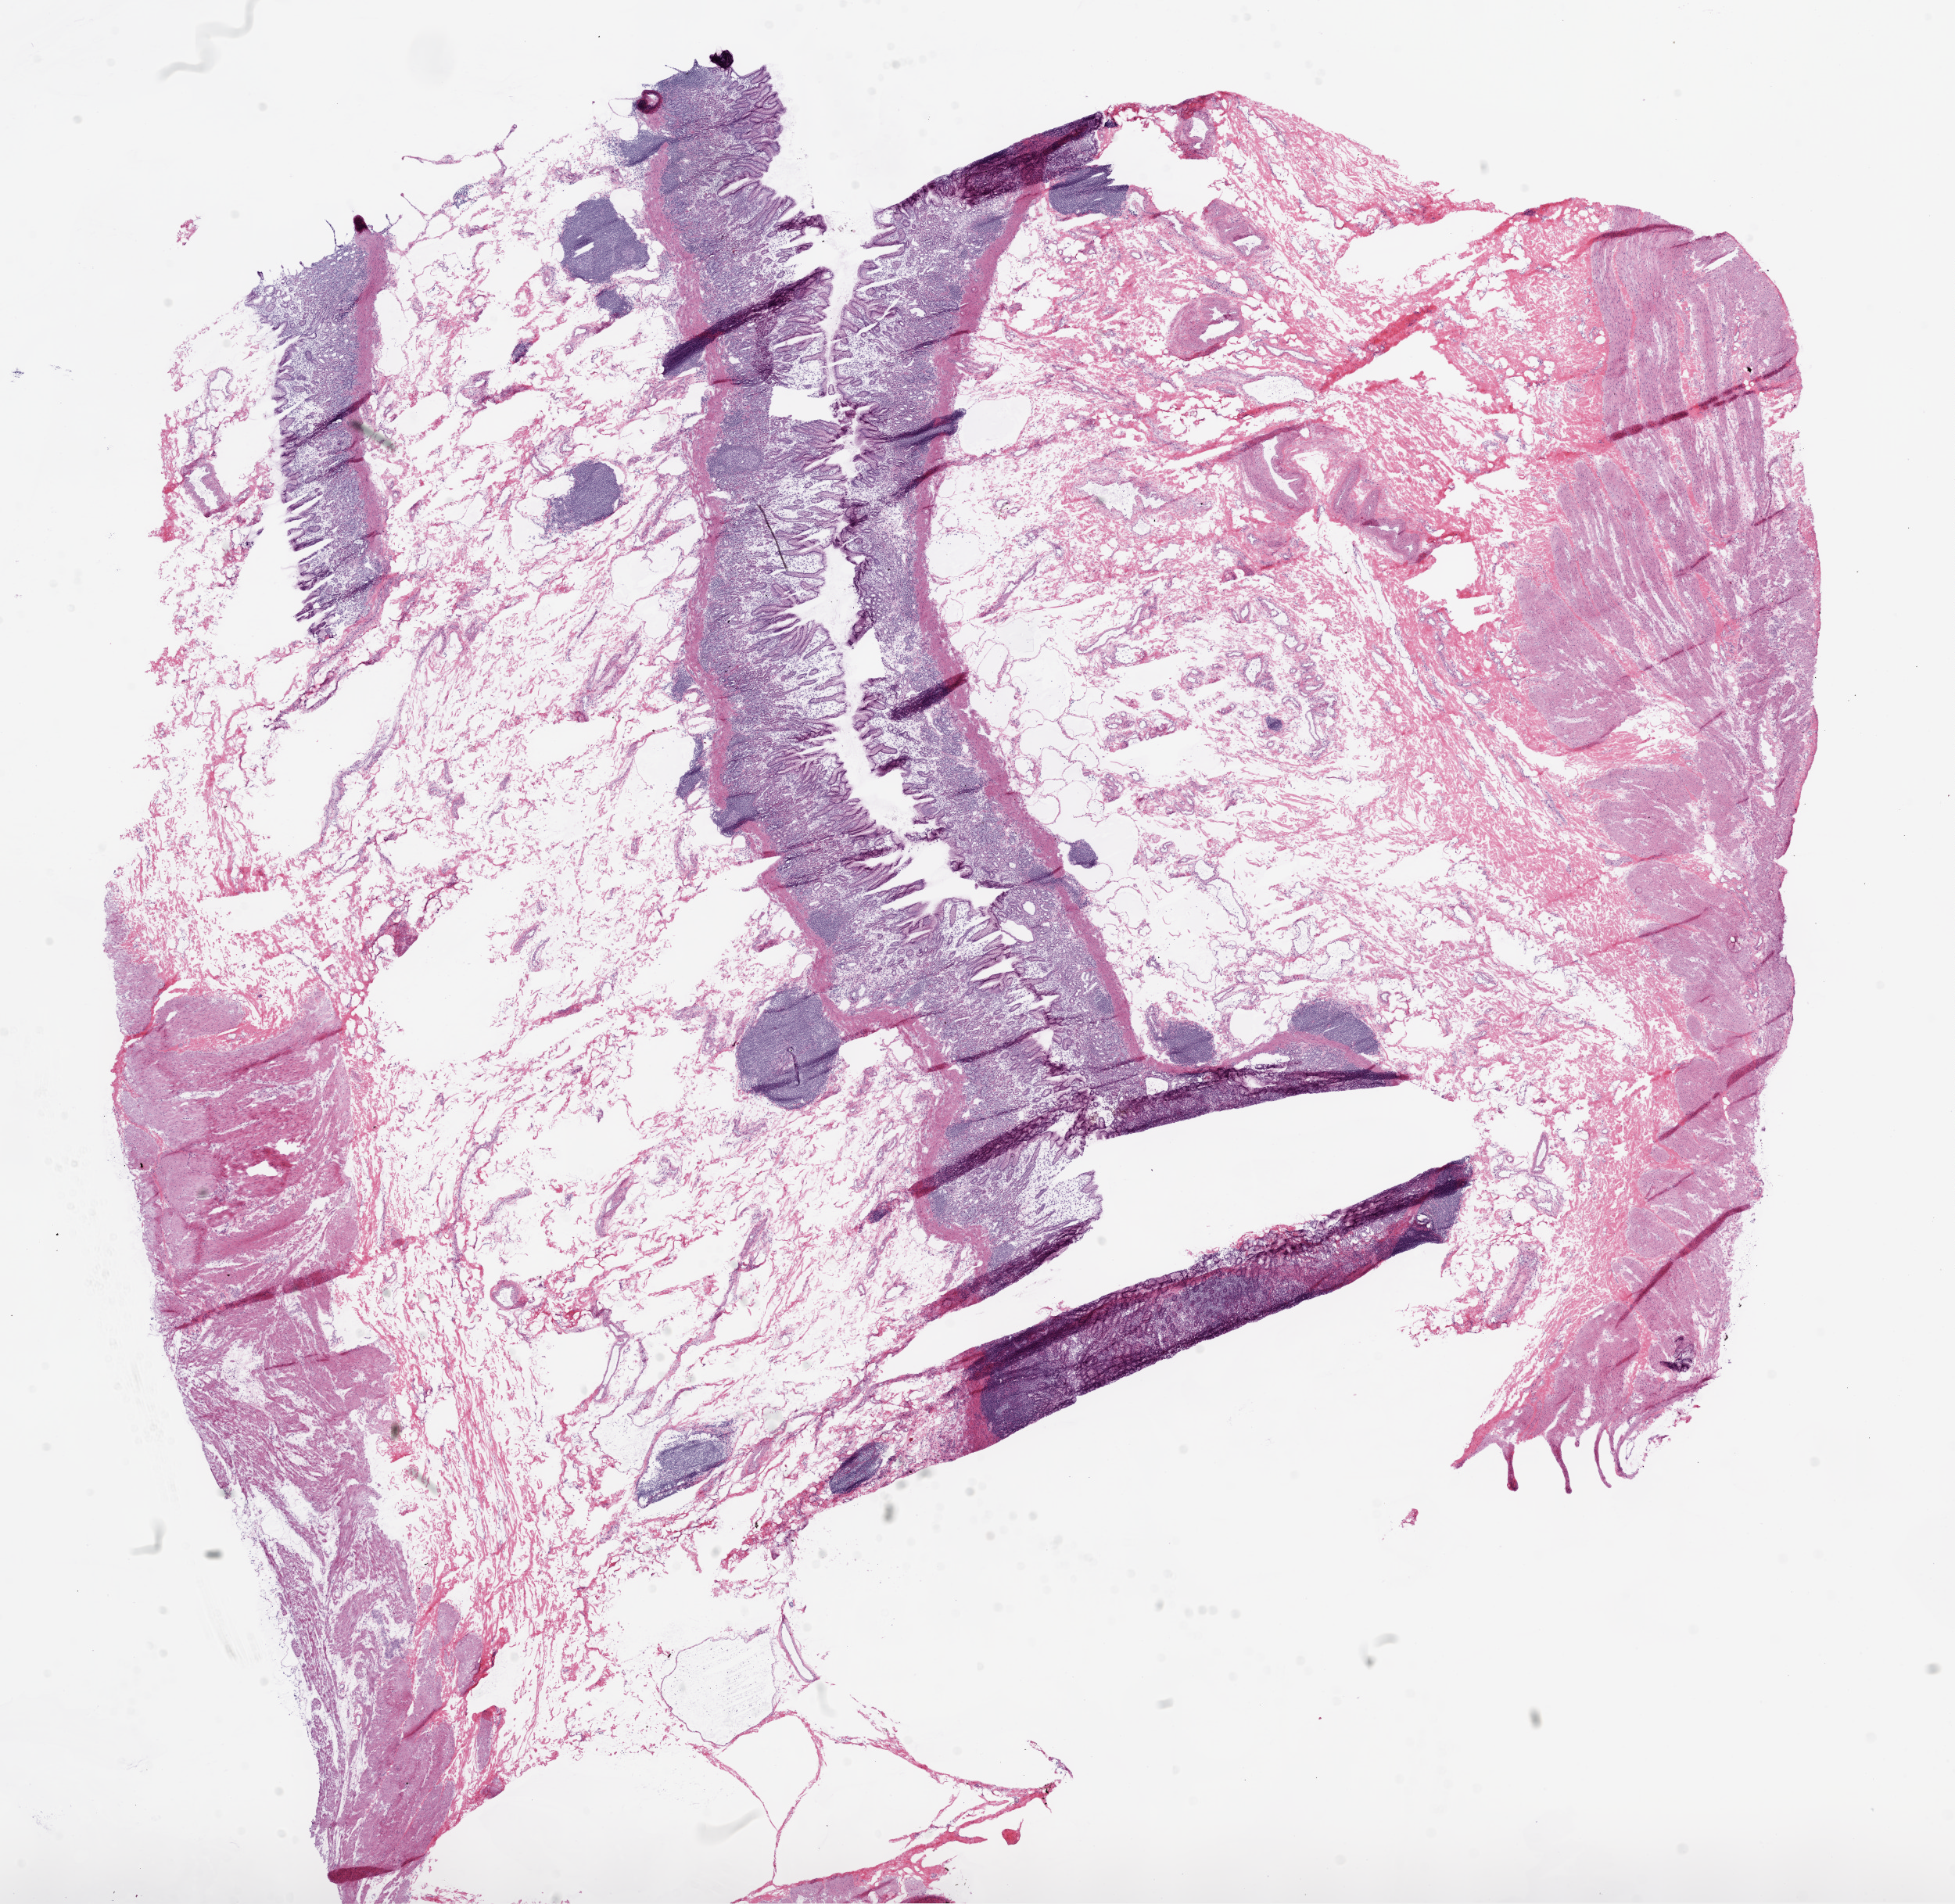
Digitized Hematoxylin and eosin (H&E) stained tissue section (whole slide), whole scanned area (about 20.1 x 19.5 mm, from a 20x scan) shown as a low-resolution overview; frozen section from the bottom of the tissue portion; sample: solid tissue normal (non-tumour tissue), stomach. Female patient; age at initial diagnosis 60 years.
This section: solid tissue normal (non-tumour) sample from the same patient. Patient diagnosis: Adenocarcinoma, NOS (body of stomach).